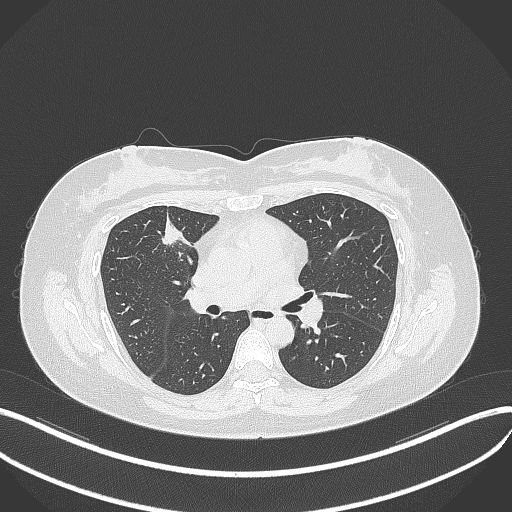
Chest CT, one axial slice. Slice 180 of 273 in the series (ordered by position). Reconstruction kernel B70f. Lung window (W 1500 / L -600 HU). 1 mm slice thickness. 512 × 512 image matrix, field of view 400 × 400 mm. Patient: female, 42 years. From the clinical record (not read from this slice): clinical TNM (as recorded): T1b N0 M0.
Structures marked on this image (rectangle marked by the reading radiologist):
- lung tumour (recorded histology: adenocarcinoma): bounding box <155,215,184,253> (left, top, right, bottom; pixels)